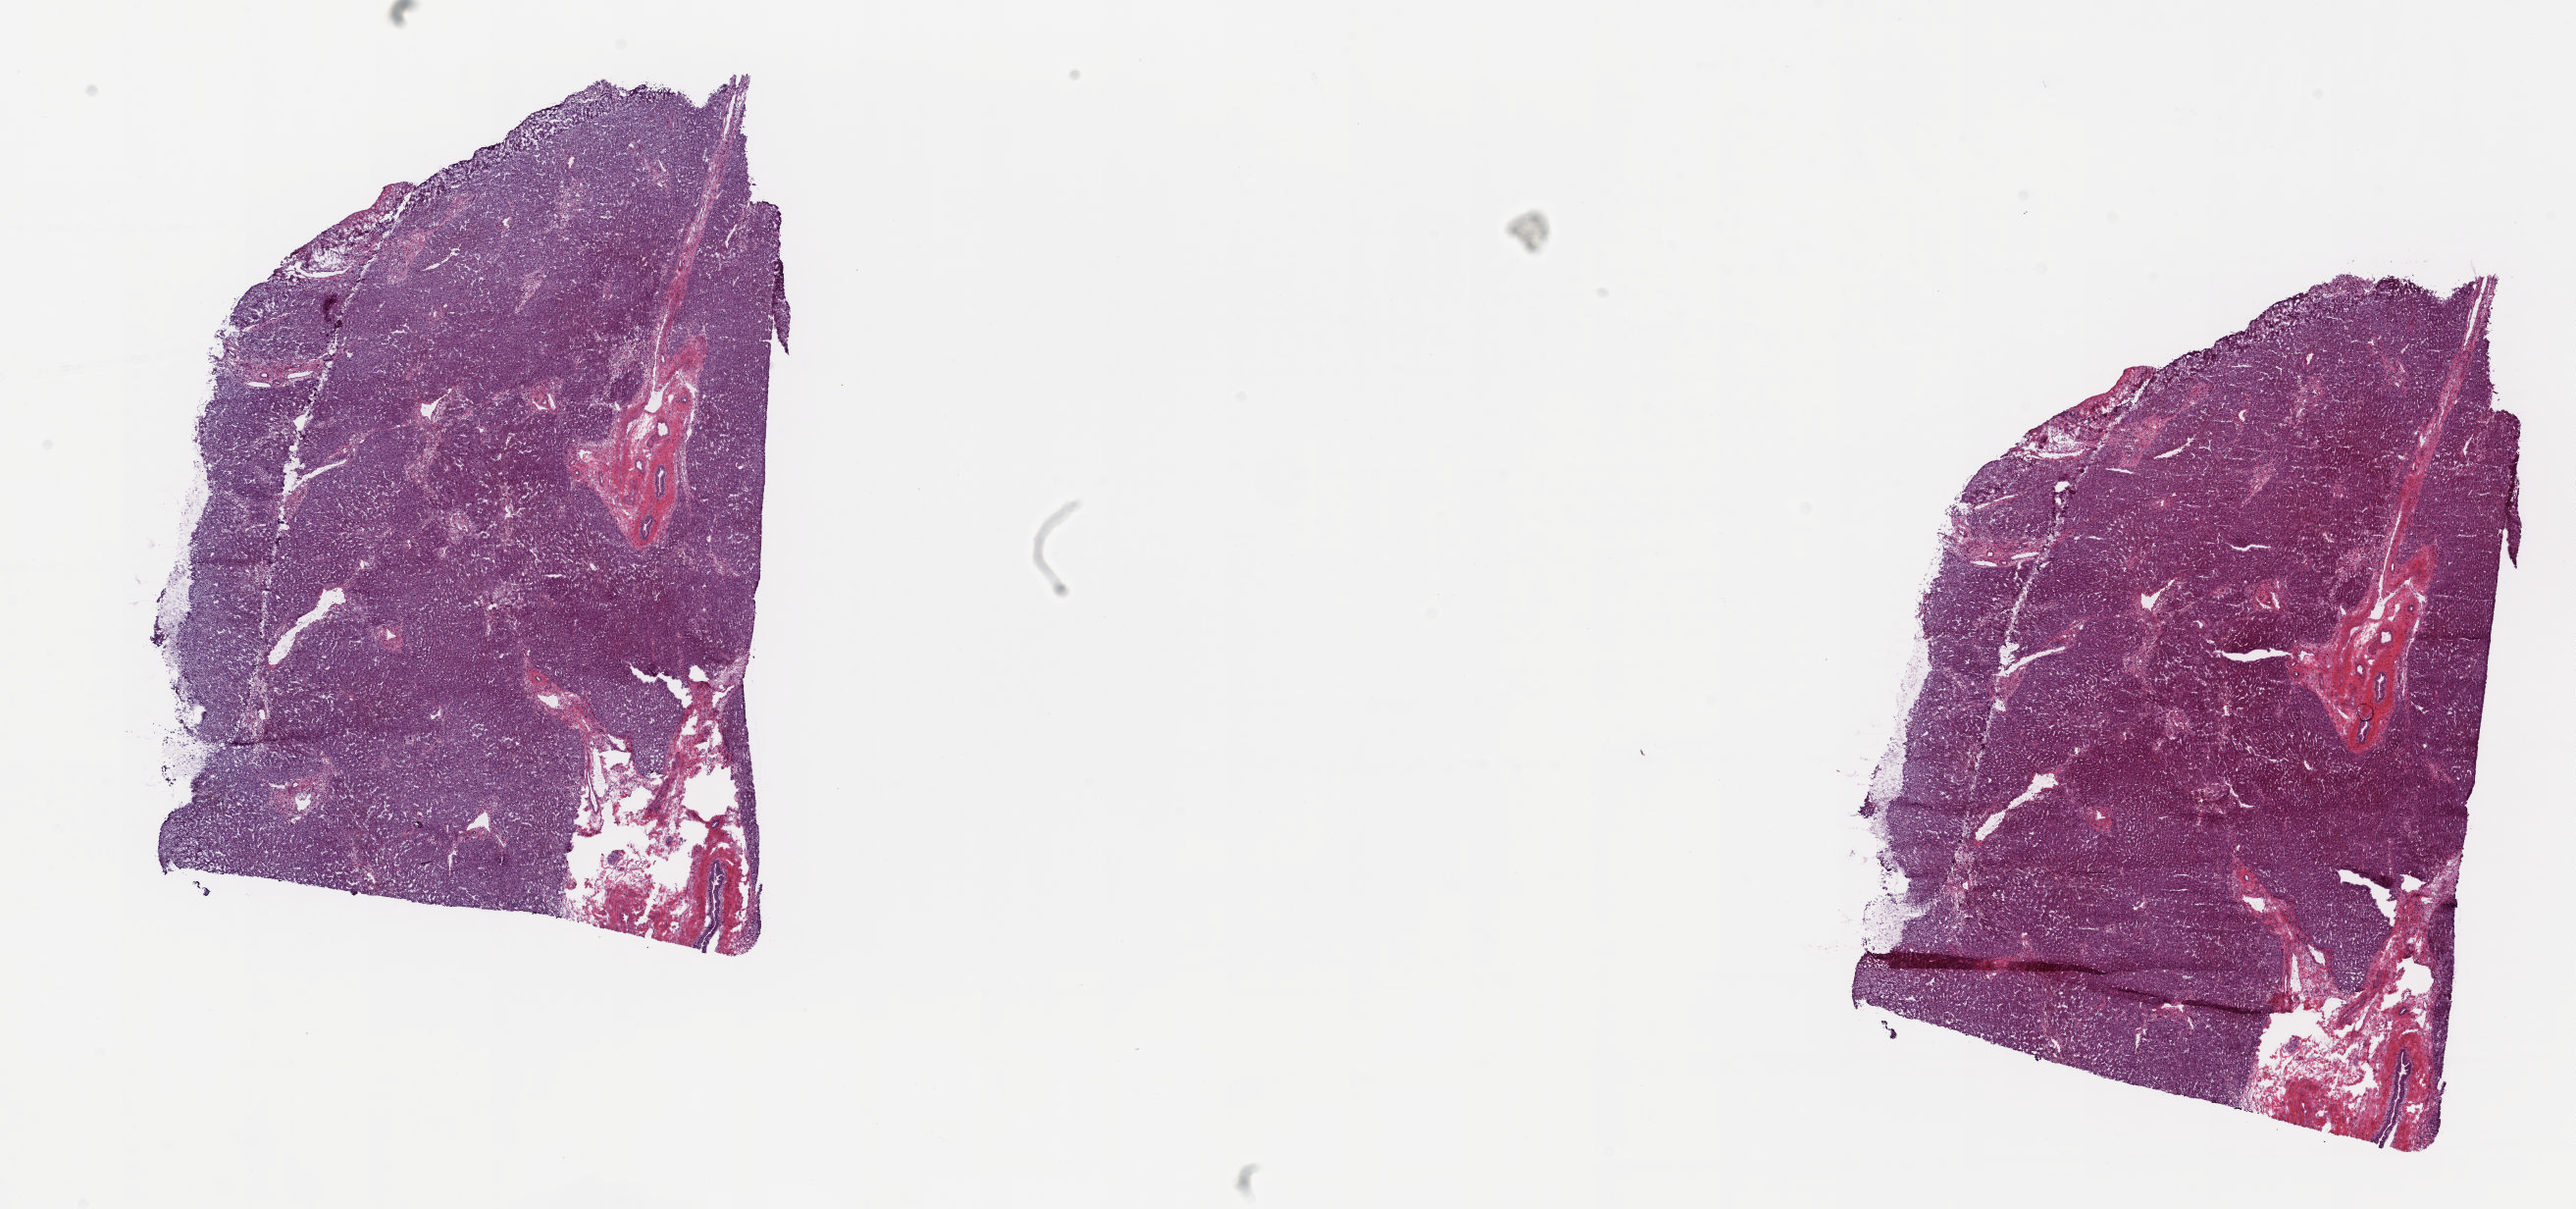
Whole-slide histology image, Hematoxylin and eosin (H&E) stained — low-resolution overview of the scanned area, about 20.8 x 9.8 mm (from a 20x scan), frozen section from the top of the tissue portion, liver, solid tissue normal (non-tumour tissue) sample. Patient: male, age at initial diagnosis 70 years. Composition of this section per pathologist review: tumour cells 0%, tumour nuclei 0%, normal cells 85%, stromal cells 15%, necrosis 0%. Inflammatory infiltration, as recorded: lymphocyte infiltration 2%, monocyte infiltration 1%, neutrophil infiltration 0%.
This section: solid tissue normal (non-tumour) sample from the same patient. Patient diagnosis: Hepatocellular carcinoma, NOS.